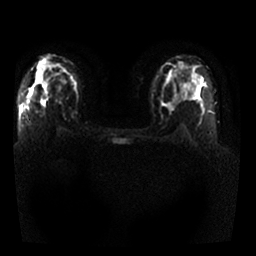
Breast MRI, one axial slice; position 16 of 25 along the scan axis; diffusion-weighted series; image 2 of 4 stored at this slice position (different b-values; order by instance number); 1.5 T; 4 mm slice thickness; 256 × 256 image matrix, field of view 330 × 330 mm. Female patient.
Structures marked on this image (manually delineated by an expert):
- tumour on diffusion-weighted imaging: bounding box <29,88,44,104> (left, top, right, bottom; pixels)